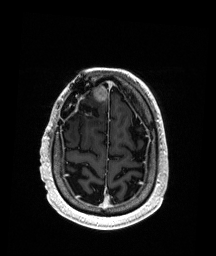
Brain MRI from a brain-tumour surgery series, one axial slice. Position 42 of 192 along the scan axis. T1-weighted post-contrast. 1 mm slice thickness. 216 × 256 image matrix. From the clinical record (not read from this slice): histopathology: Astrocytoma; WHO grade: 3; IDH mutation: yes; tumour location: Right Frontal.
Annotated regions visible in this slice (outlined manually by an expert reader):
- previous resection cavity: bounding box [x1, y1, x2, y2] px = [70, 104, 100, 126]
- tumour: [93, 85, 109, 102]